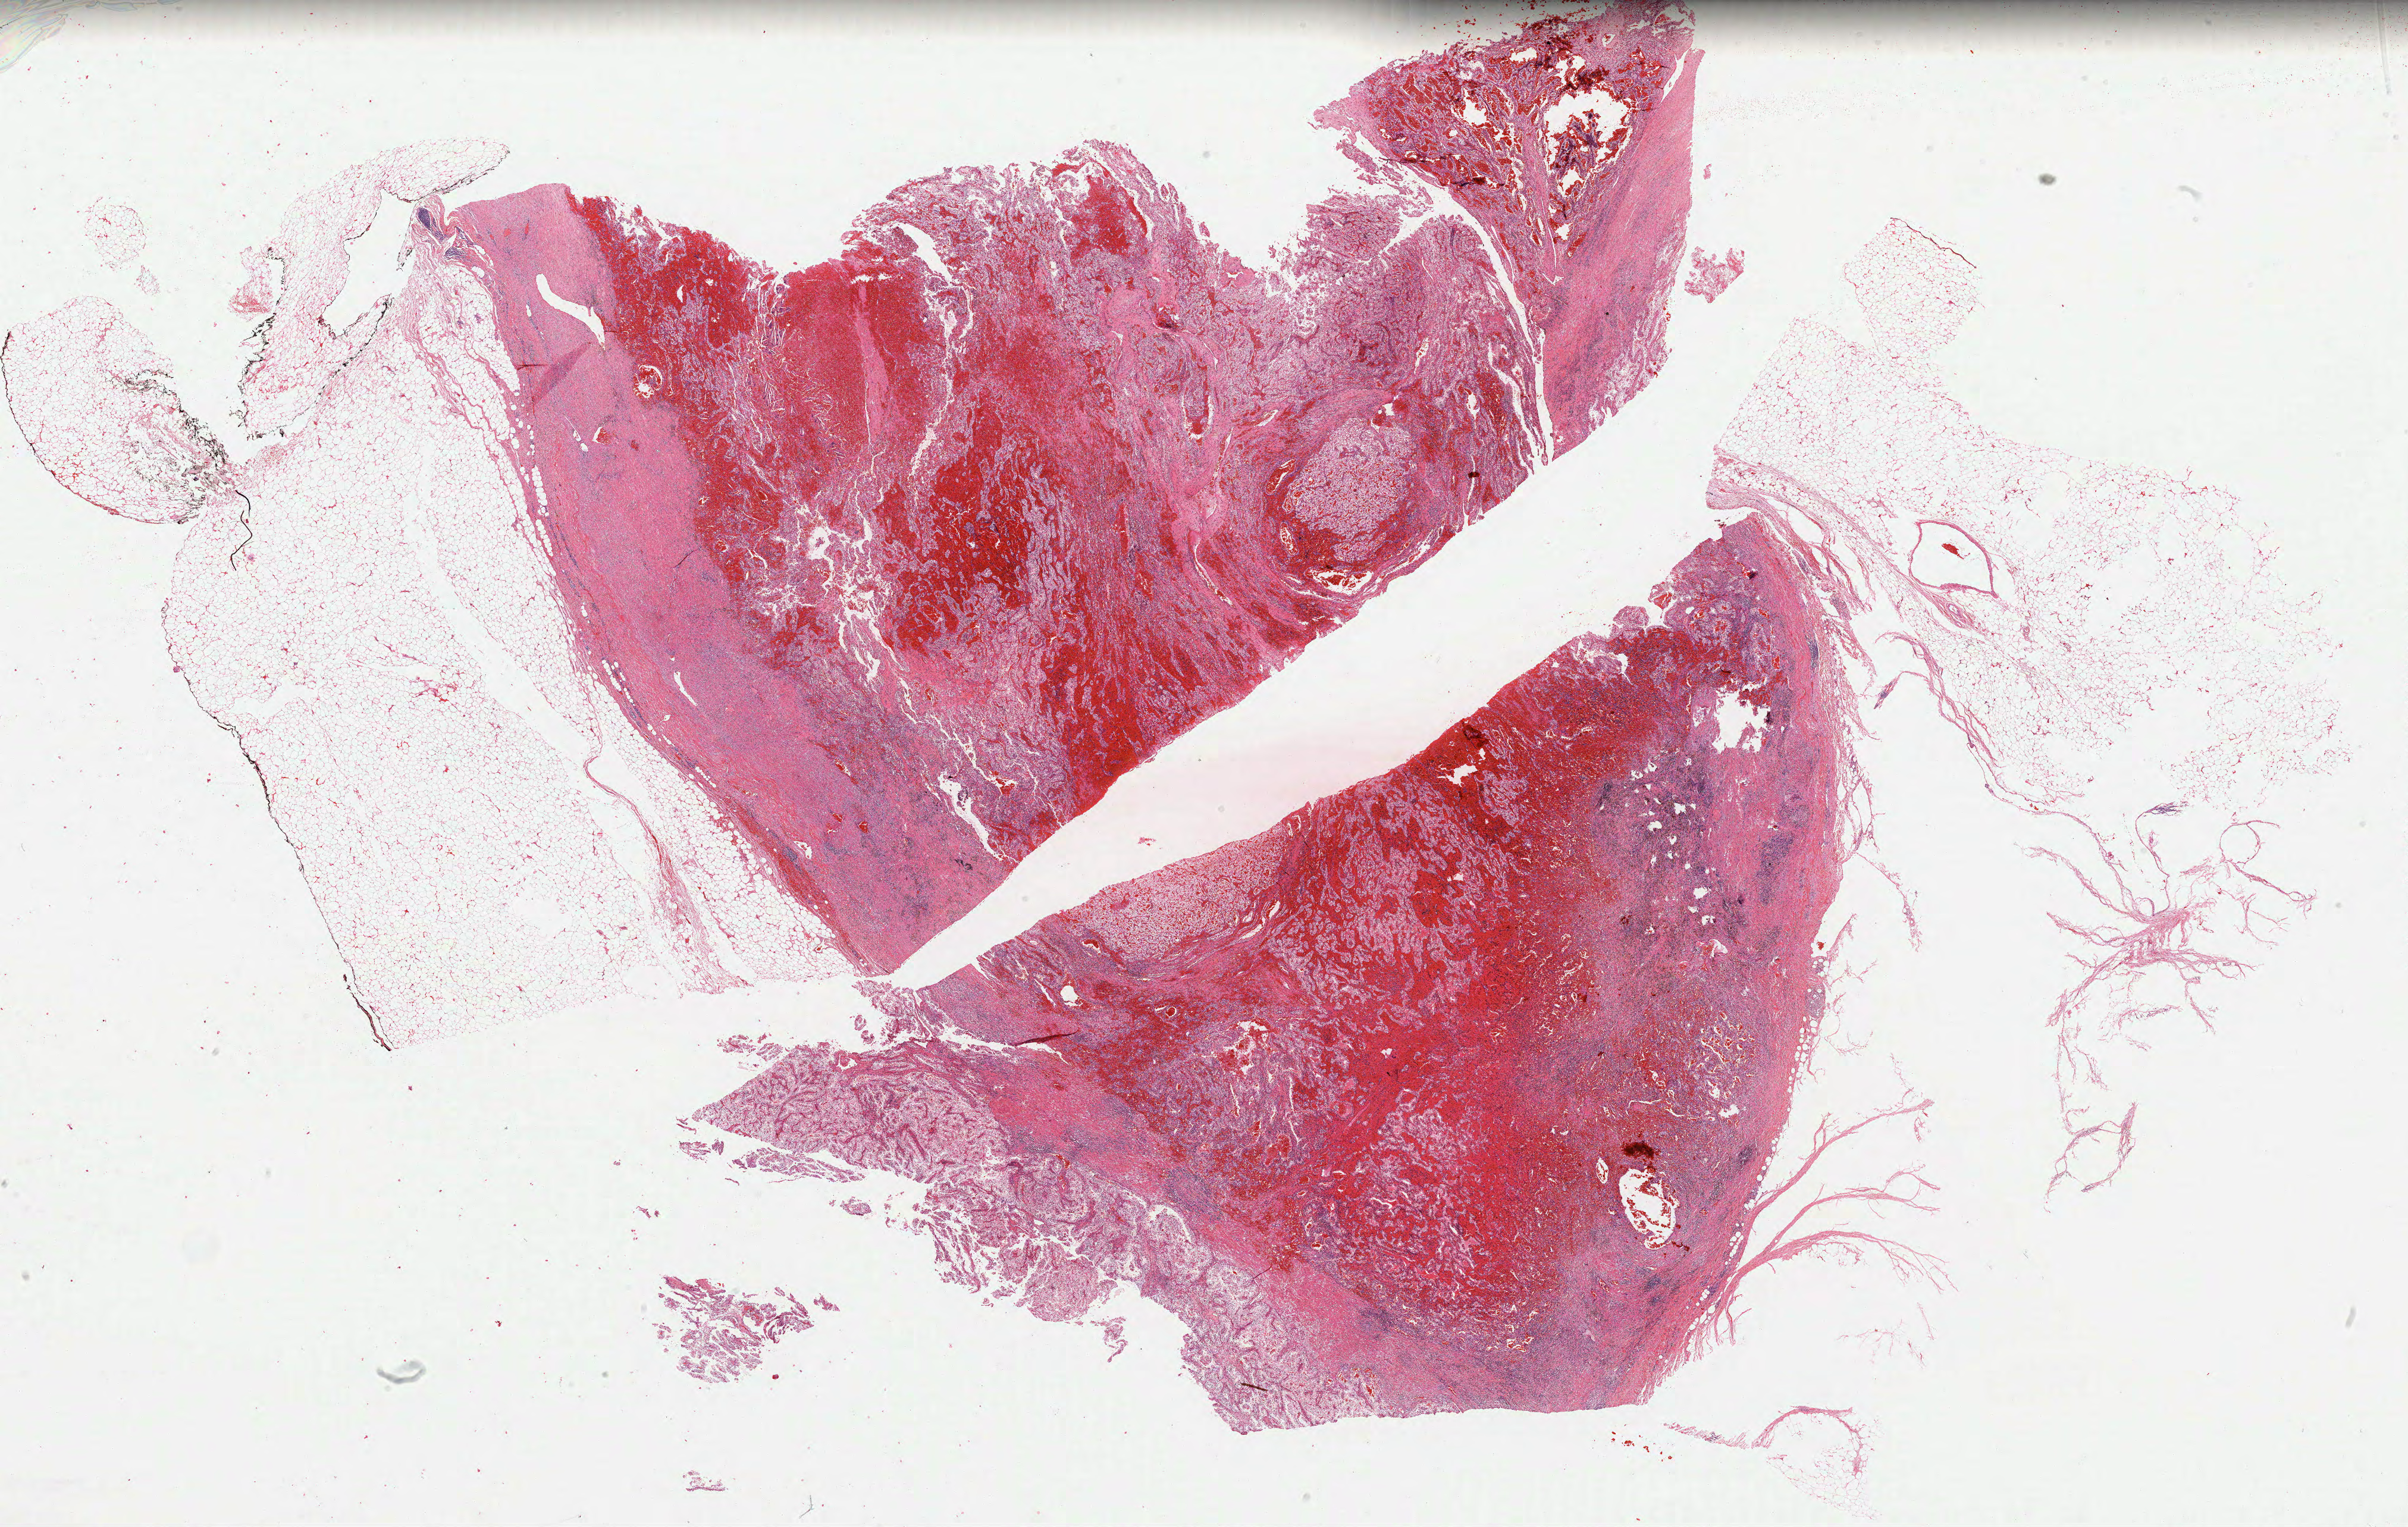
Whole-slide histology image, H&E — shown as a low-resolution overview of the whole scanned area (about 32.6 x 20.7 mm); formalin-fixed paraffin-embedded (FFPE) diagnostic section; primary tumour sample from the kidney. Patient: male, age at initial diagnosis 58 years.
Histologic diagnosis: Clear cell adenocarcinoma, NOS.